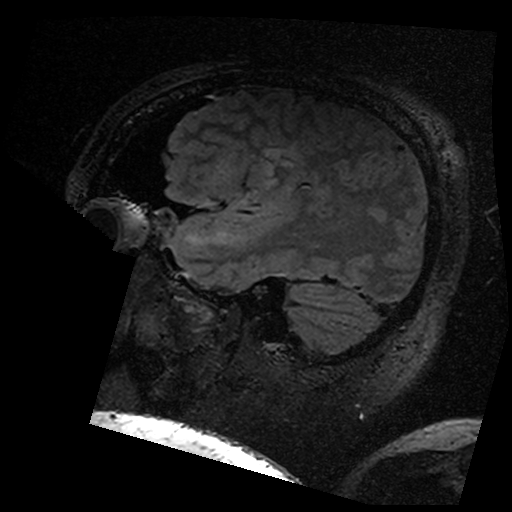
Brain MRI from a brain-tumour surgery series, one sagittal slice; position 130 of 176 along the scan axis; T2 FLAIR; 1 mm slice thickness; 512 × 512 image matrix. From the clinical record (not read from this slice): histopathology: Astrocytoma; WHO grade: 3; IDH mutation: yes; tumour location: Left Insular.
Annotated regions visible in this slice (manually delineated by an expert):
- residual tumour: bounding box <277,154,294,165> (left, top, right, bottom; pixels)